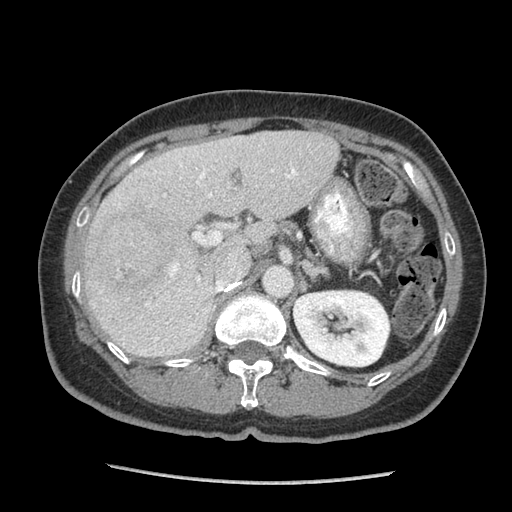
Contrast-enhanced abdominal CT (liver protocol), one axial slice; slice 50 of 105 in the series (ordered by position); reconstruction kernel STANDARD; soft-tissue window (W 400 / L 40 HU); 2.5 mm slice thickness; 512 × 512 image matrix, field of view 340 × 340 mm. From the clinical record (not read from this slice): diagnosis: hepatocellular carcinoma (patient treated with transarterial chemoembolisation; whether this scan precedes or follows treatment is not stated here); TNM stage (as recorded): Stage-I.
Annotated regions visible in this slice (semi-automatically segmented with operator editing):
- liver parenchyma outside the tumour (the mass and vessels are separate outlines, so this box may not span the whole liver): bounding box <84,130,338,356> (left, top, right, bottom; pixels)
- mass: <86,202,184,296>
- liver vessels: <142,153,297,352>